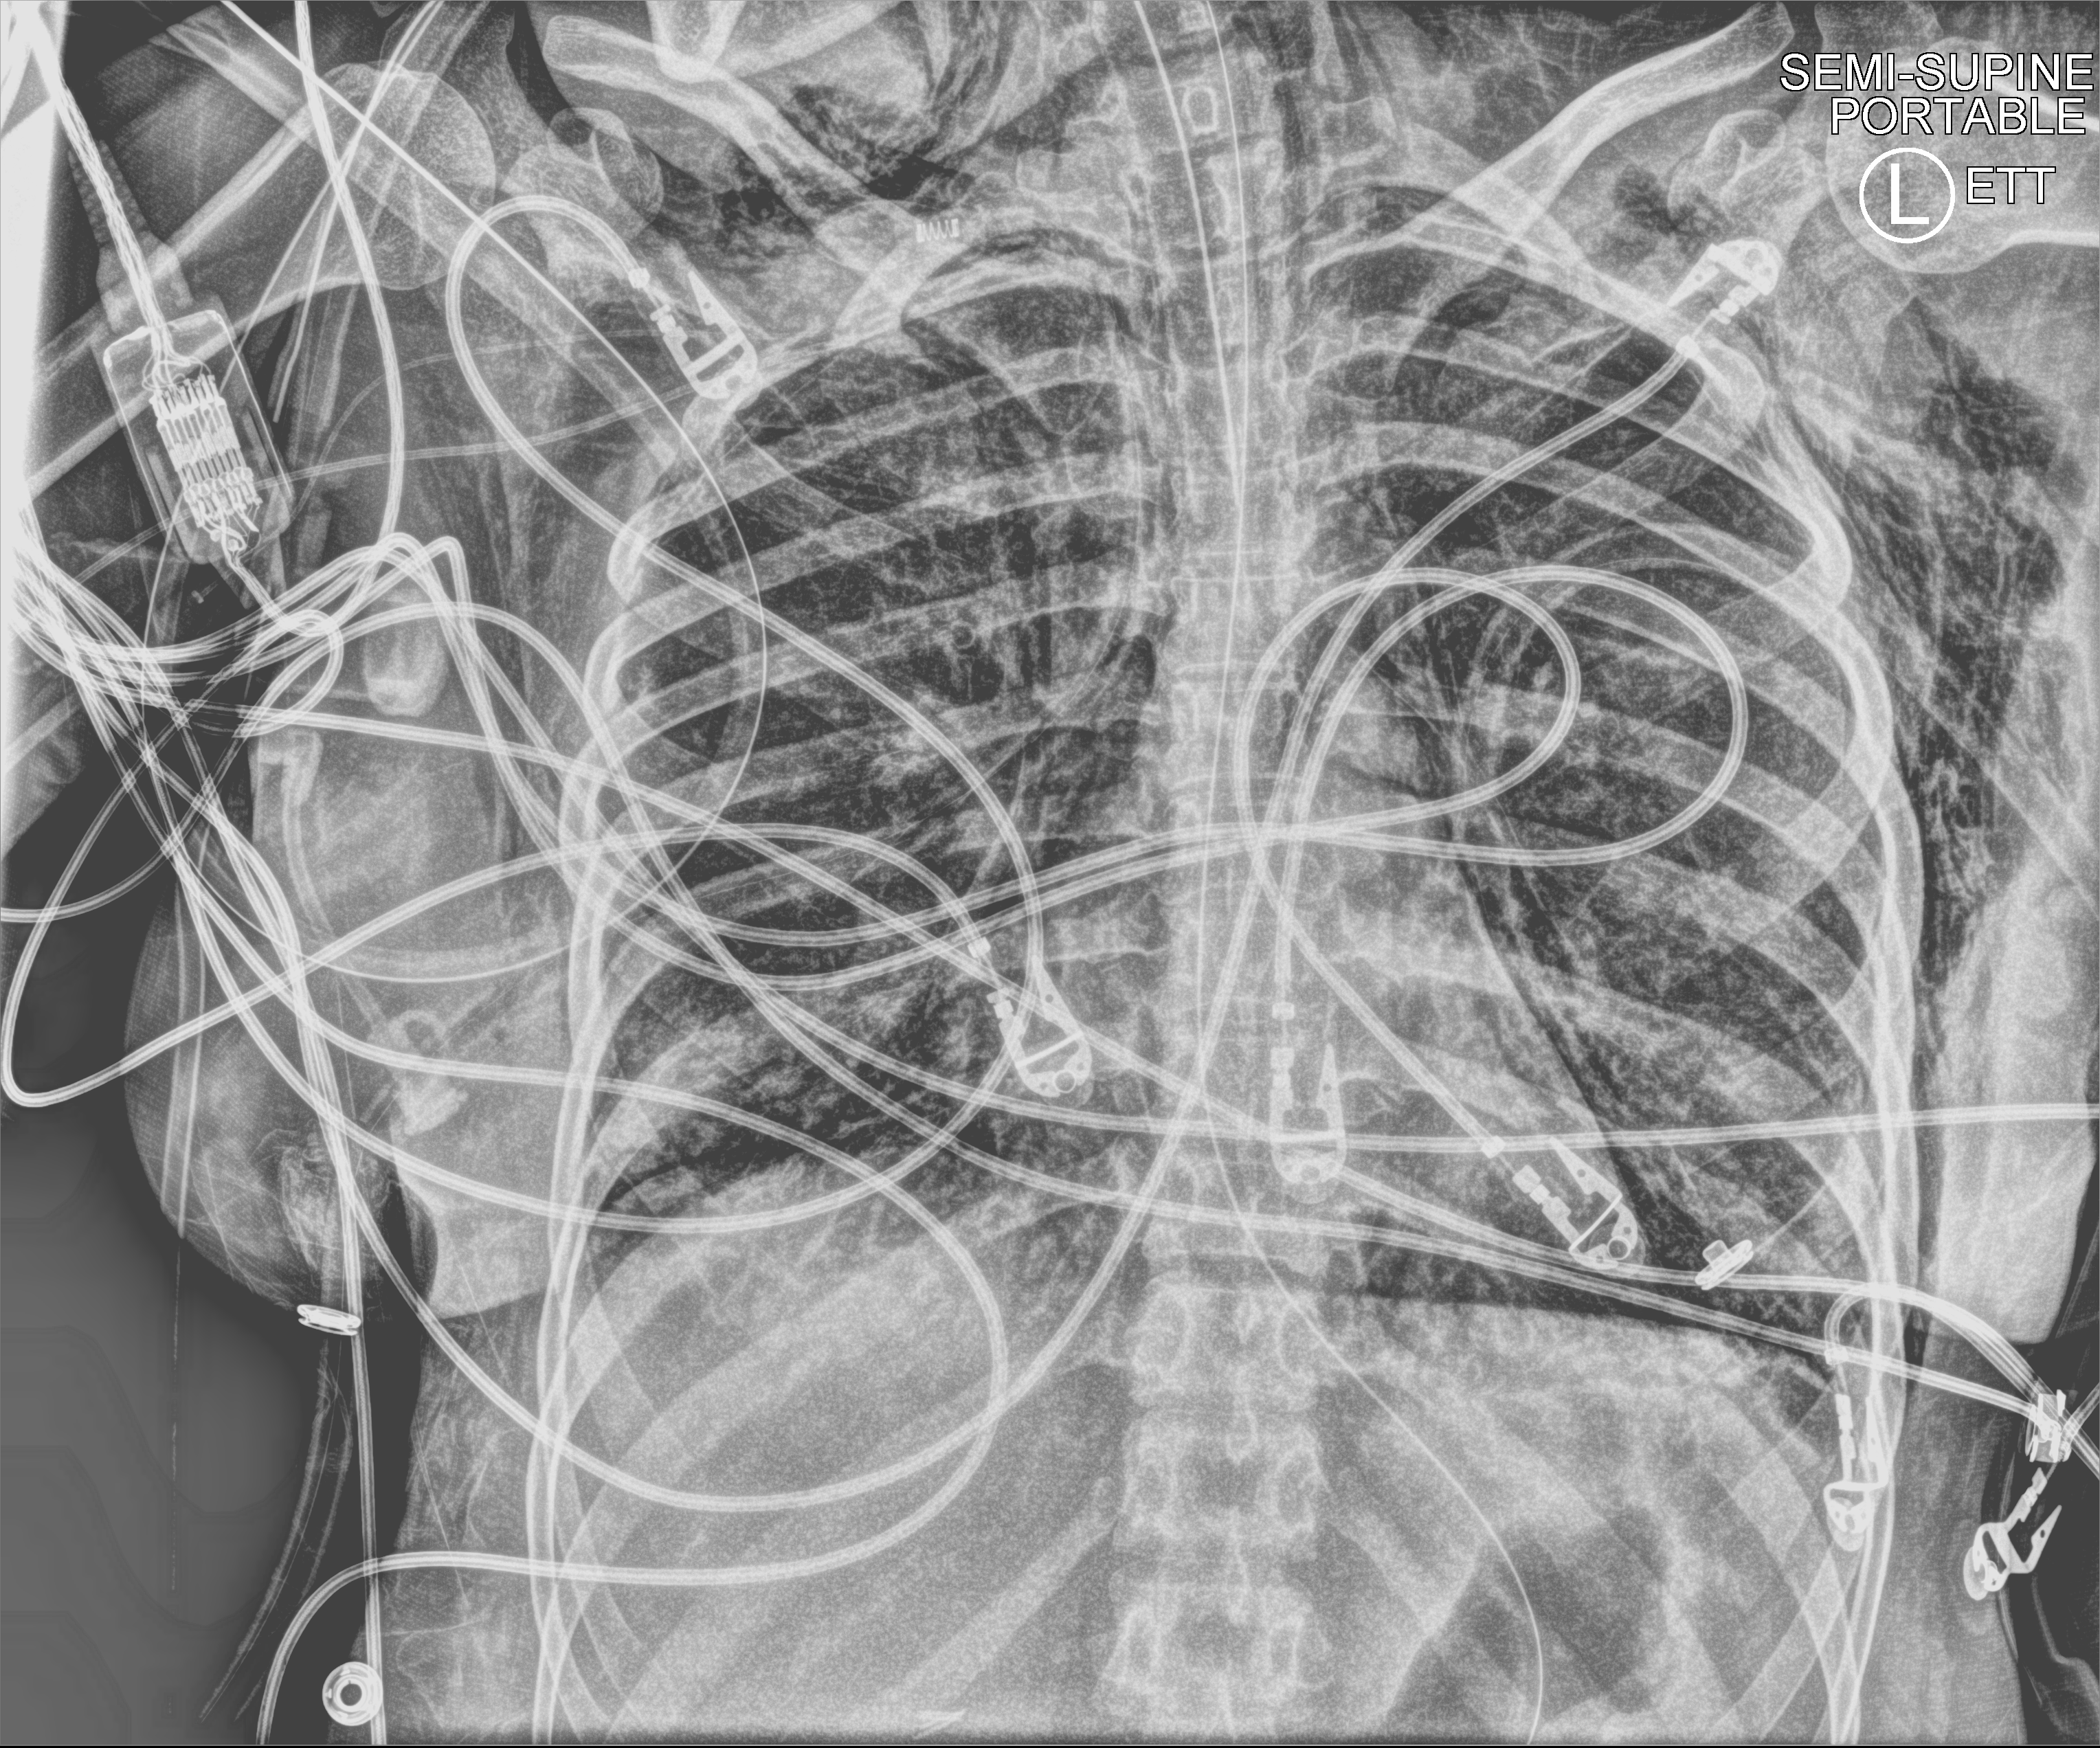
Chest X-ray (portable). Adult patient hospitalised with COVID-19, age 18–59 years.
Admission-level facts for this patient (not findings on this image; timing relative to this image not recorded): mechanically ventilated during this hospital stay: yes.